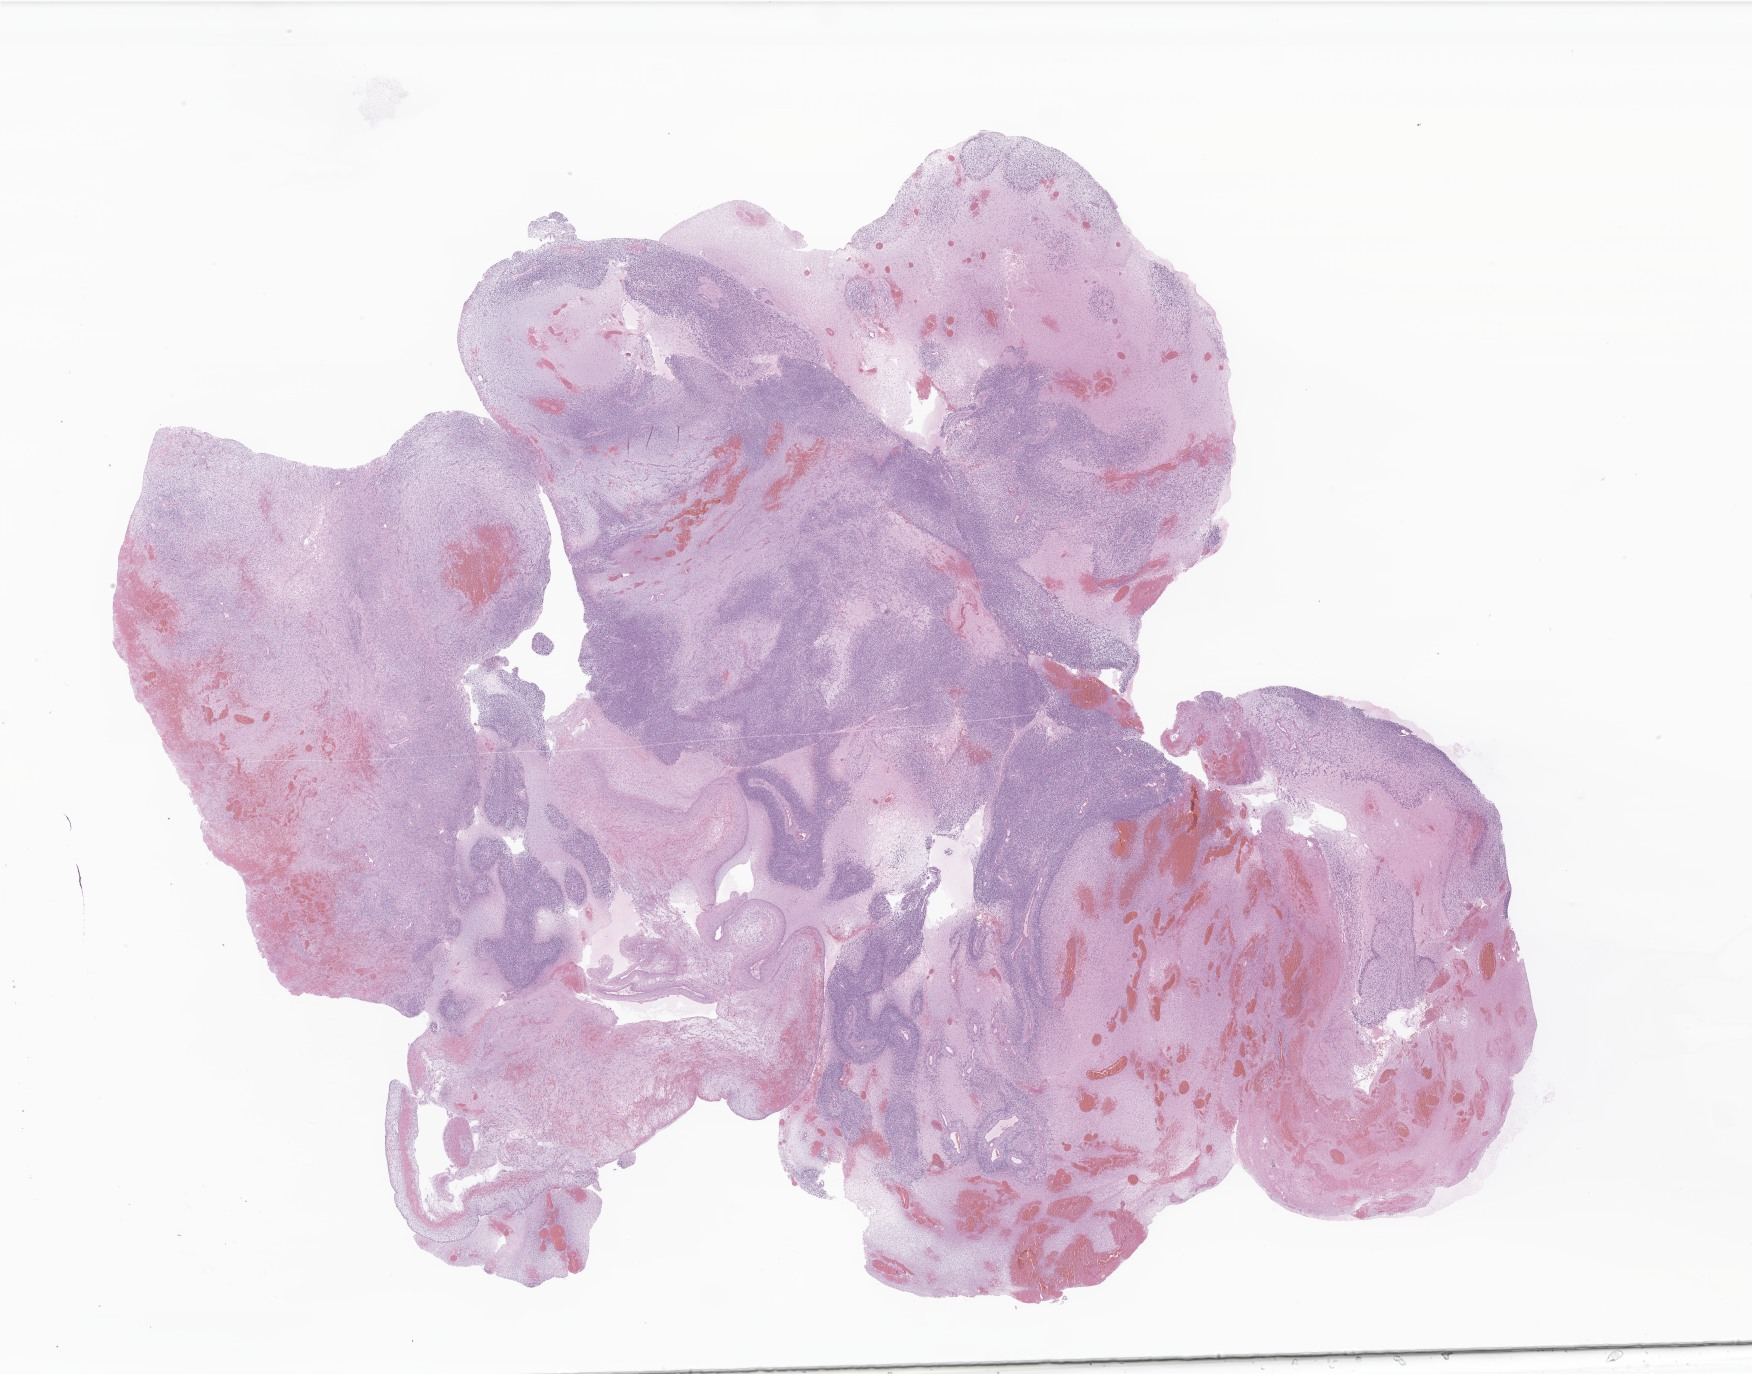
Whole-slide image, H&E stain of tumor tissue from the scrotum — shown as a low-resolution overview of the whole scanned area (about 29.6 x 23.2 mm), formalin-fixed paraffin-embedded section. Patient: male, age 169 months.
Diagnosis (ICD-O-3 morphology term): Embryonal rhabdomyosarcoma, NOS.